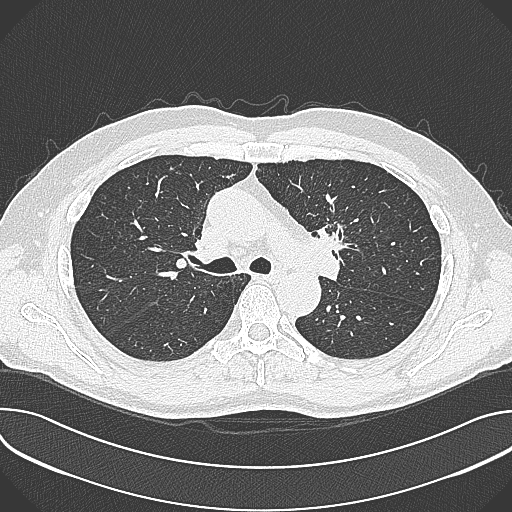
Axial slice from a low-dose chest CT screening exam; baseline screening round; lung window (W 1500 / L -600 HU); 1 mm slice thickness; lung (sharp) reconstruction kernel (B80f); slice 119 of 361 in the series; 512 × 512 image matrix. Male participant, aged 59 years at enrolment.
Lesion marked by an expert reader, bounding box (x1, y1, x2, y2) in pixels: (303, 191, 366, 257). The screening reader recorded 2 non-calcified nodules or masses ≥4 mm on this exam; which of them this box marks is not recorded. Lung cancer was diagnosed 21 days after this screen: non-small cell carcinoma, left upper lobe, poorly differentiated (G3), stage IIIA (AJCC 6th edition), 35 mm at pathology.